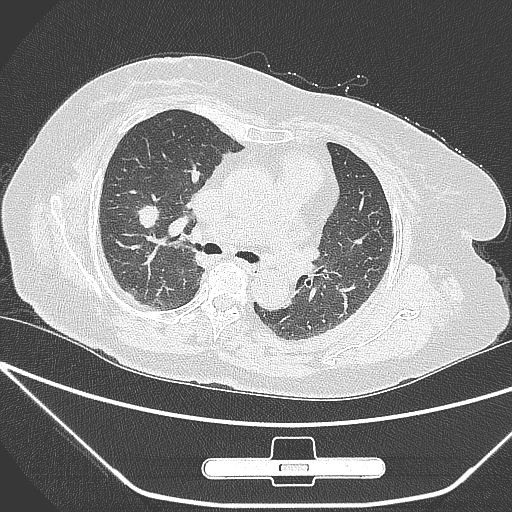
Chest CT, one axial slice. Position 163 of 245 along the scan axis. 120 kVp. Lung window (W 1500 / L -600 HU). 1 mm slice thickness. 512 × 512 image matrix. Female patient, age 65 years. Case-level facts recorded for this patient, not image findings: clinical TNM (as recorded): T1c N0 M0.
Annotated regions visible in this slice (rectangle marked by the reading radiologist):
- lung tumour (recorded histology: adenocarcinoma): box from (x=131, y=194) to (x=167, y=239) px